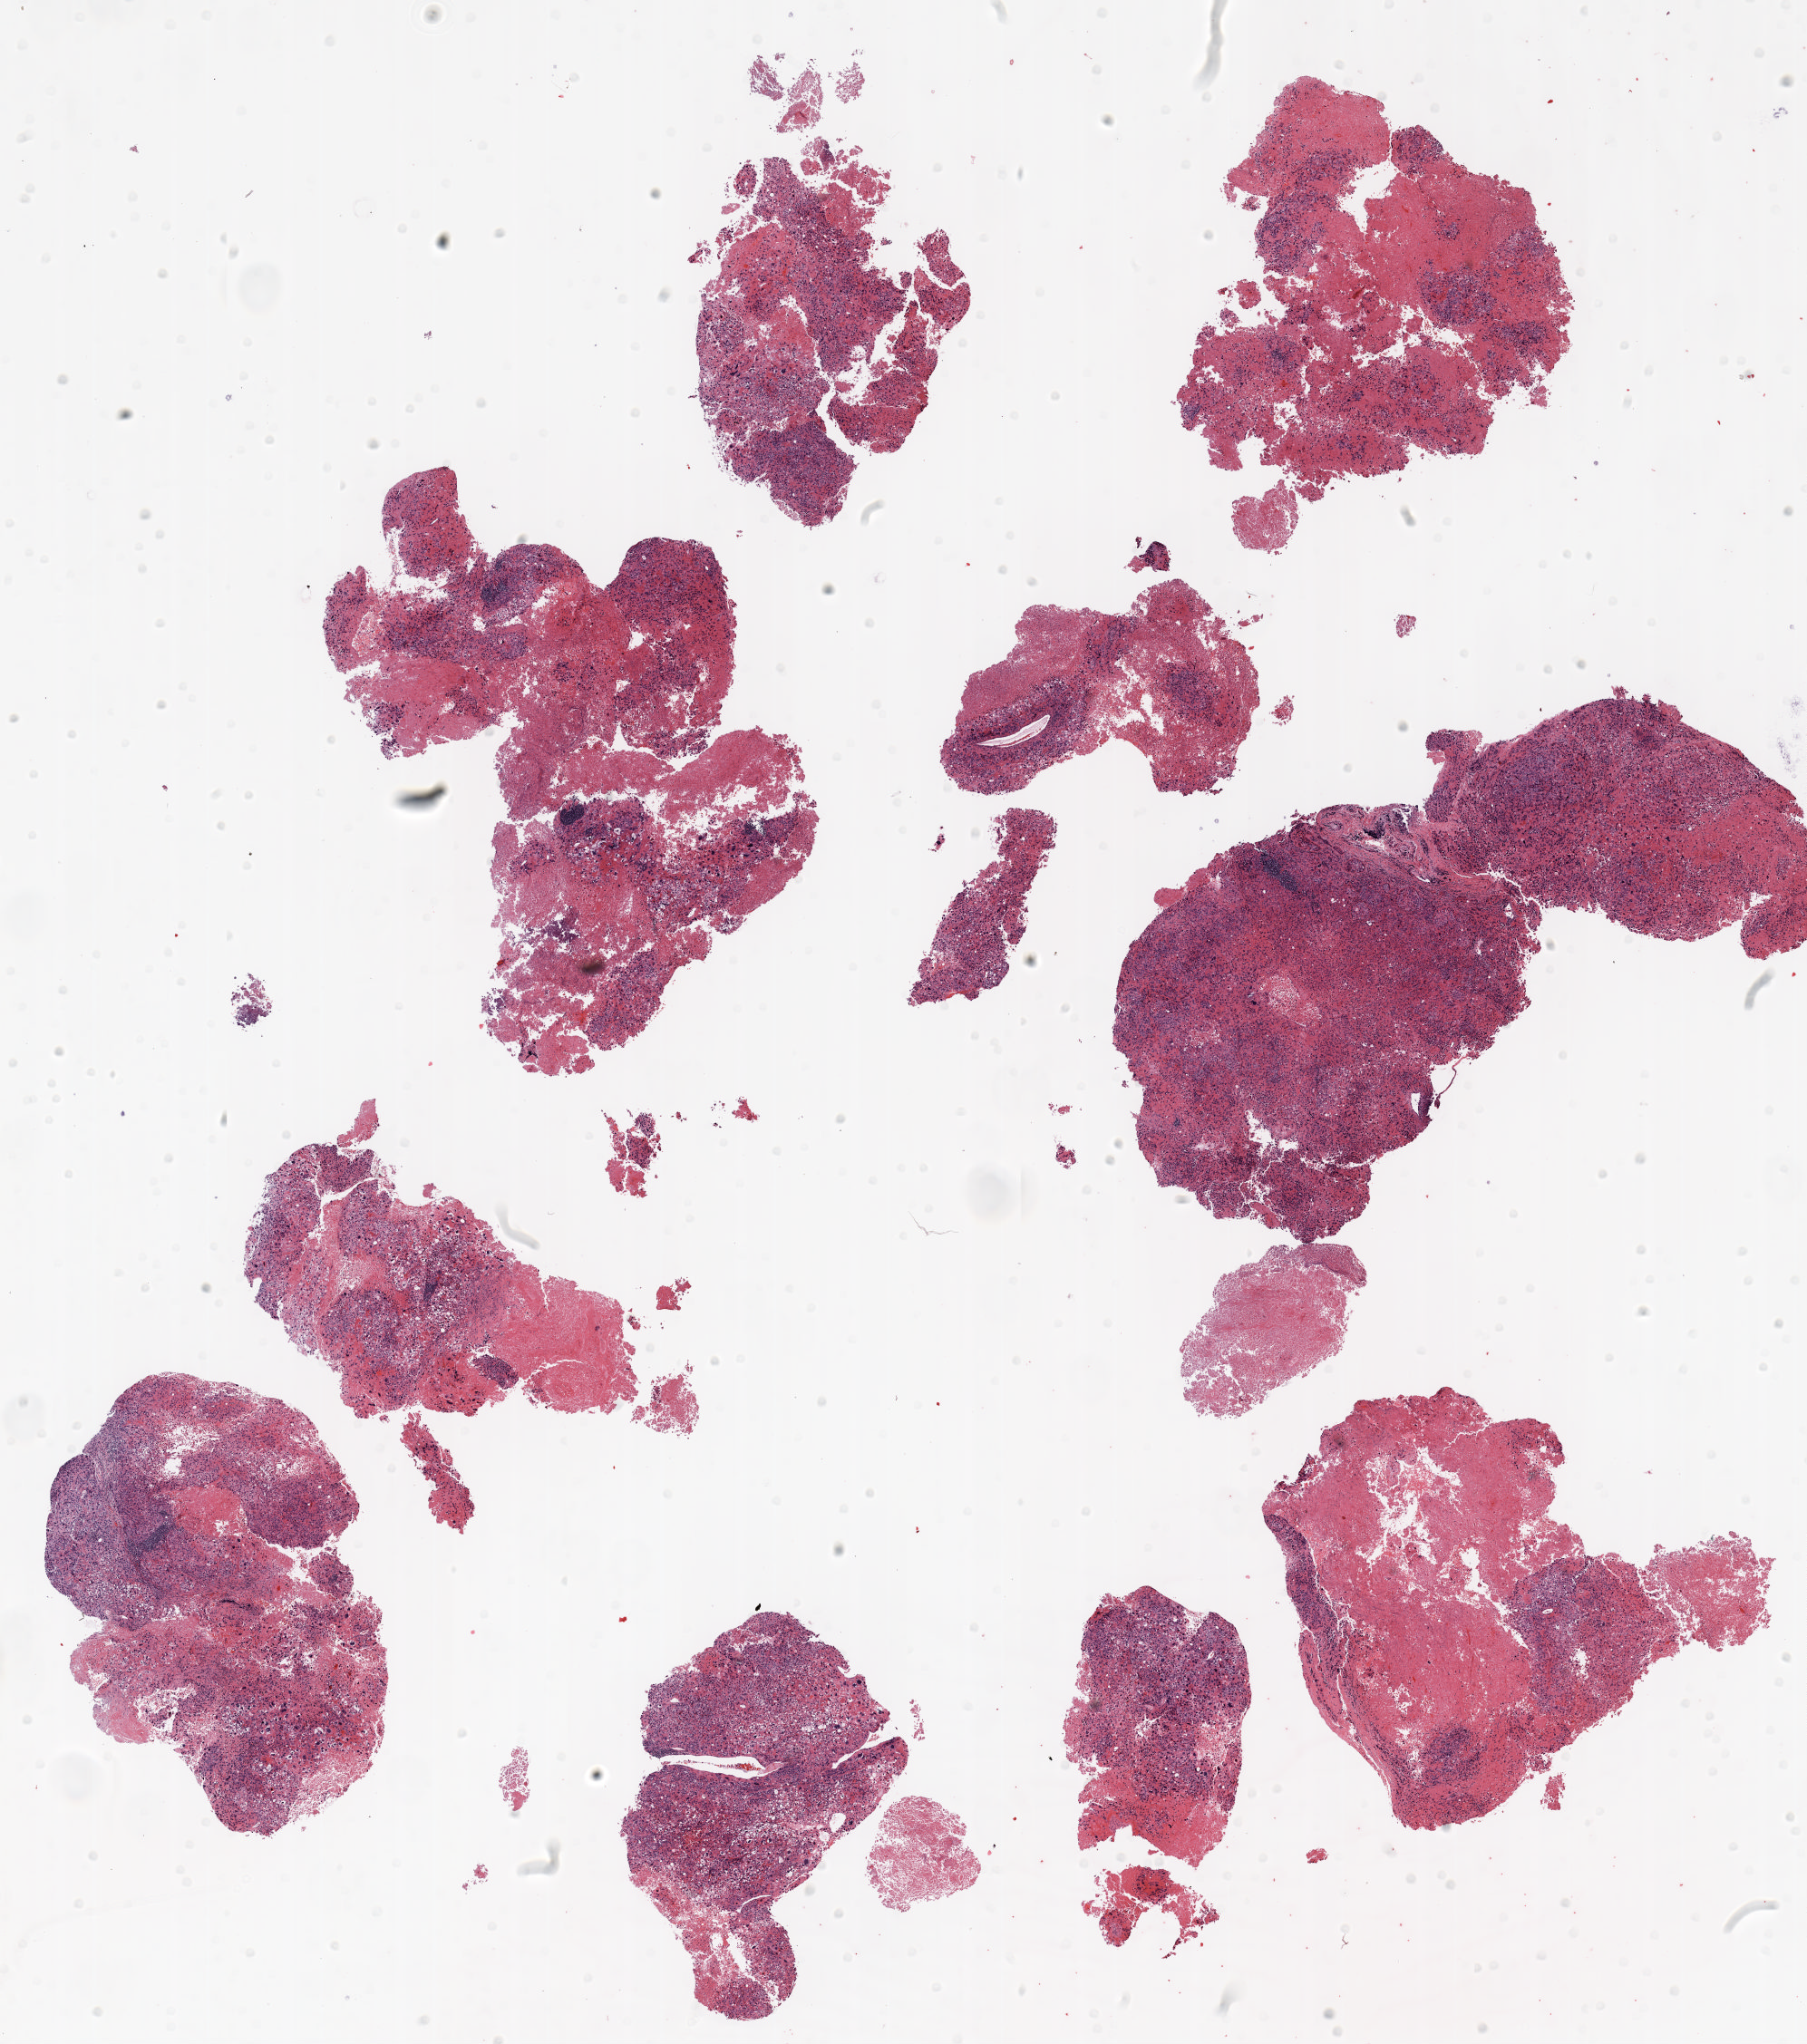
Whole-slide histology image, Hematoxylin and eosin (H&E) stained, low-resolution overview of the scanned area, about 16.0 x 18.1 mm, FFPE section, lung. Female patient, aged 61 at enrolment. Current smoker at enrolment. Grade: cannot be assessed (GX).
Tumour size (pathology): 25 mm. Stage (AJCC 6th edition): IIIB. Primary tumour location (clinical record): right upper lobe. Participant's lung-cancer diagnosis: Adenosquamous carcinoma. ICD-O-3 topography: upper lobe of lung (C34.1).